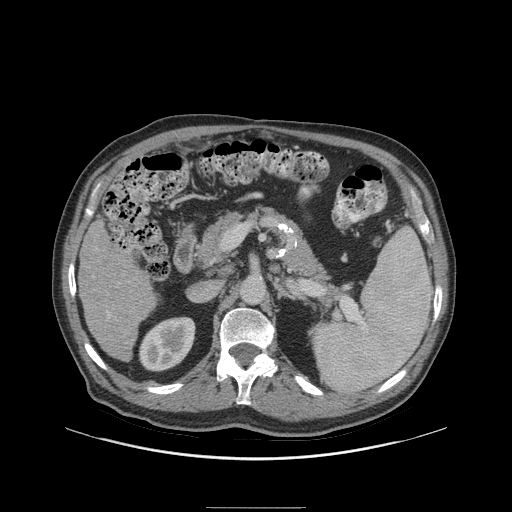
Contrast-enhanced abdominal CT (liver protocol), one axial slice. 140 kVp. Soft-tissue window (W 400 / L 40 HU). 2.5 mm slice thickness. 512 × 512 image matrix, field of view 440 × 440 mm. From the clinical record (not read from this slice): diagnosis: hepatocellular carcinoma (patient treated with transarterial chemoembolisation; whether this scan precedes or follows treatment is not stated here); TNM stage (as recorded): Stage-I; Child-Pugh class: A; tumour nodularity: uninodular; tumour size: 5.1 cm.
Structures marked on this image (semi-automatically segmented with operator editing):
- liver parenchyma outside the tumour (the mass and vessels are separate outlines, so this box may not span the whole liver): box from (x=78, y=220) to (x=156, y=360) px
- liver vessels: (x=108, y=313)–(x=110, y=316)